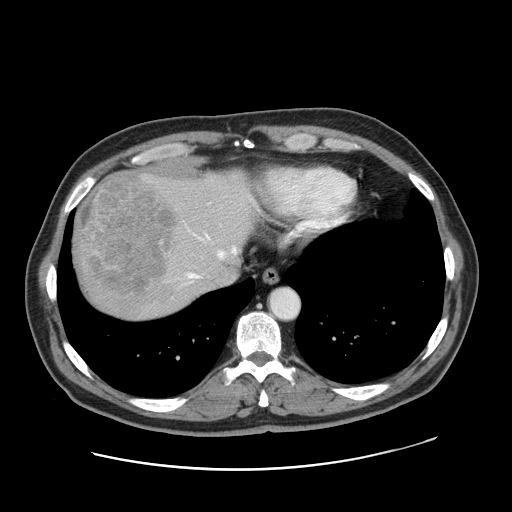
Contrast-enhanced abdominal CT, one axial slice. Position 140 of 178 along the scan axis. 120 kVp. Intravenous contrast given. Soft-tissue window (W 400 / L 40 HU). 2.5 mm slice thickness. 512 × 512 image matrix, field of view 403 × 403 mm. Male patient, age 63 years. From the clinical record (not read from this slice): diagnosis: colorectal cancer liver metastases, imaged before liver resection; multiple liver metastases: yes; largest metastasis: 8 cm; chemotherapy before resection: no.
Annotated regions visible in this slice (expert manual segmentation):
- hepatic veins: bounding box [x1, y1, x2, y2] px = [188, 233, 239, 278]
- liver: [73, 169, 259, 321]
- planned liver remnant (the part of the liver to remain after resection): [177, 171, 258, 280]
- portal vein (with intrahepatic branches): [160, 240, 162, 242]
- liver metastasis: [75, 175, 174, 299]